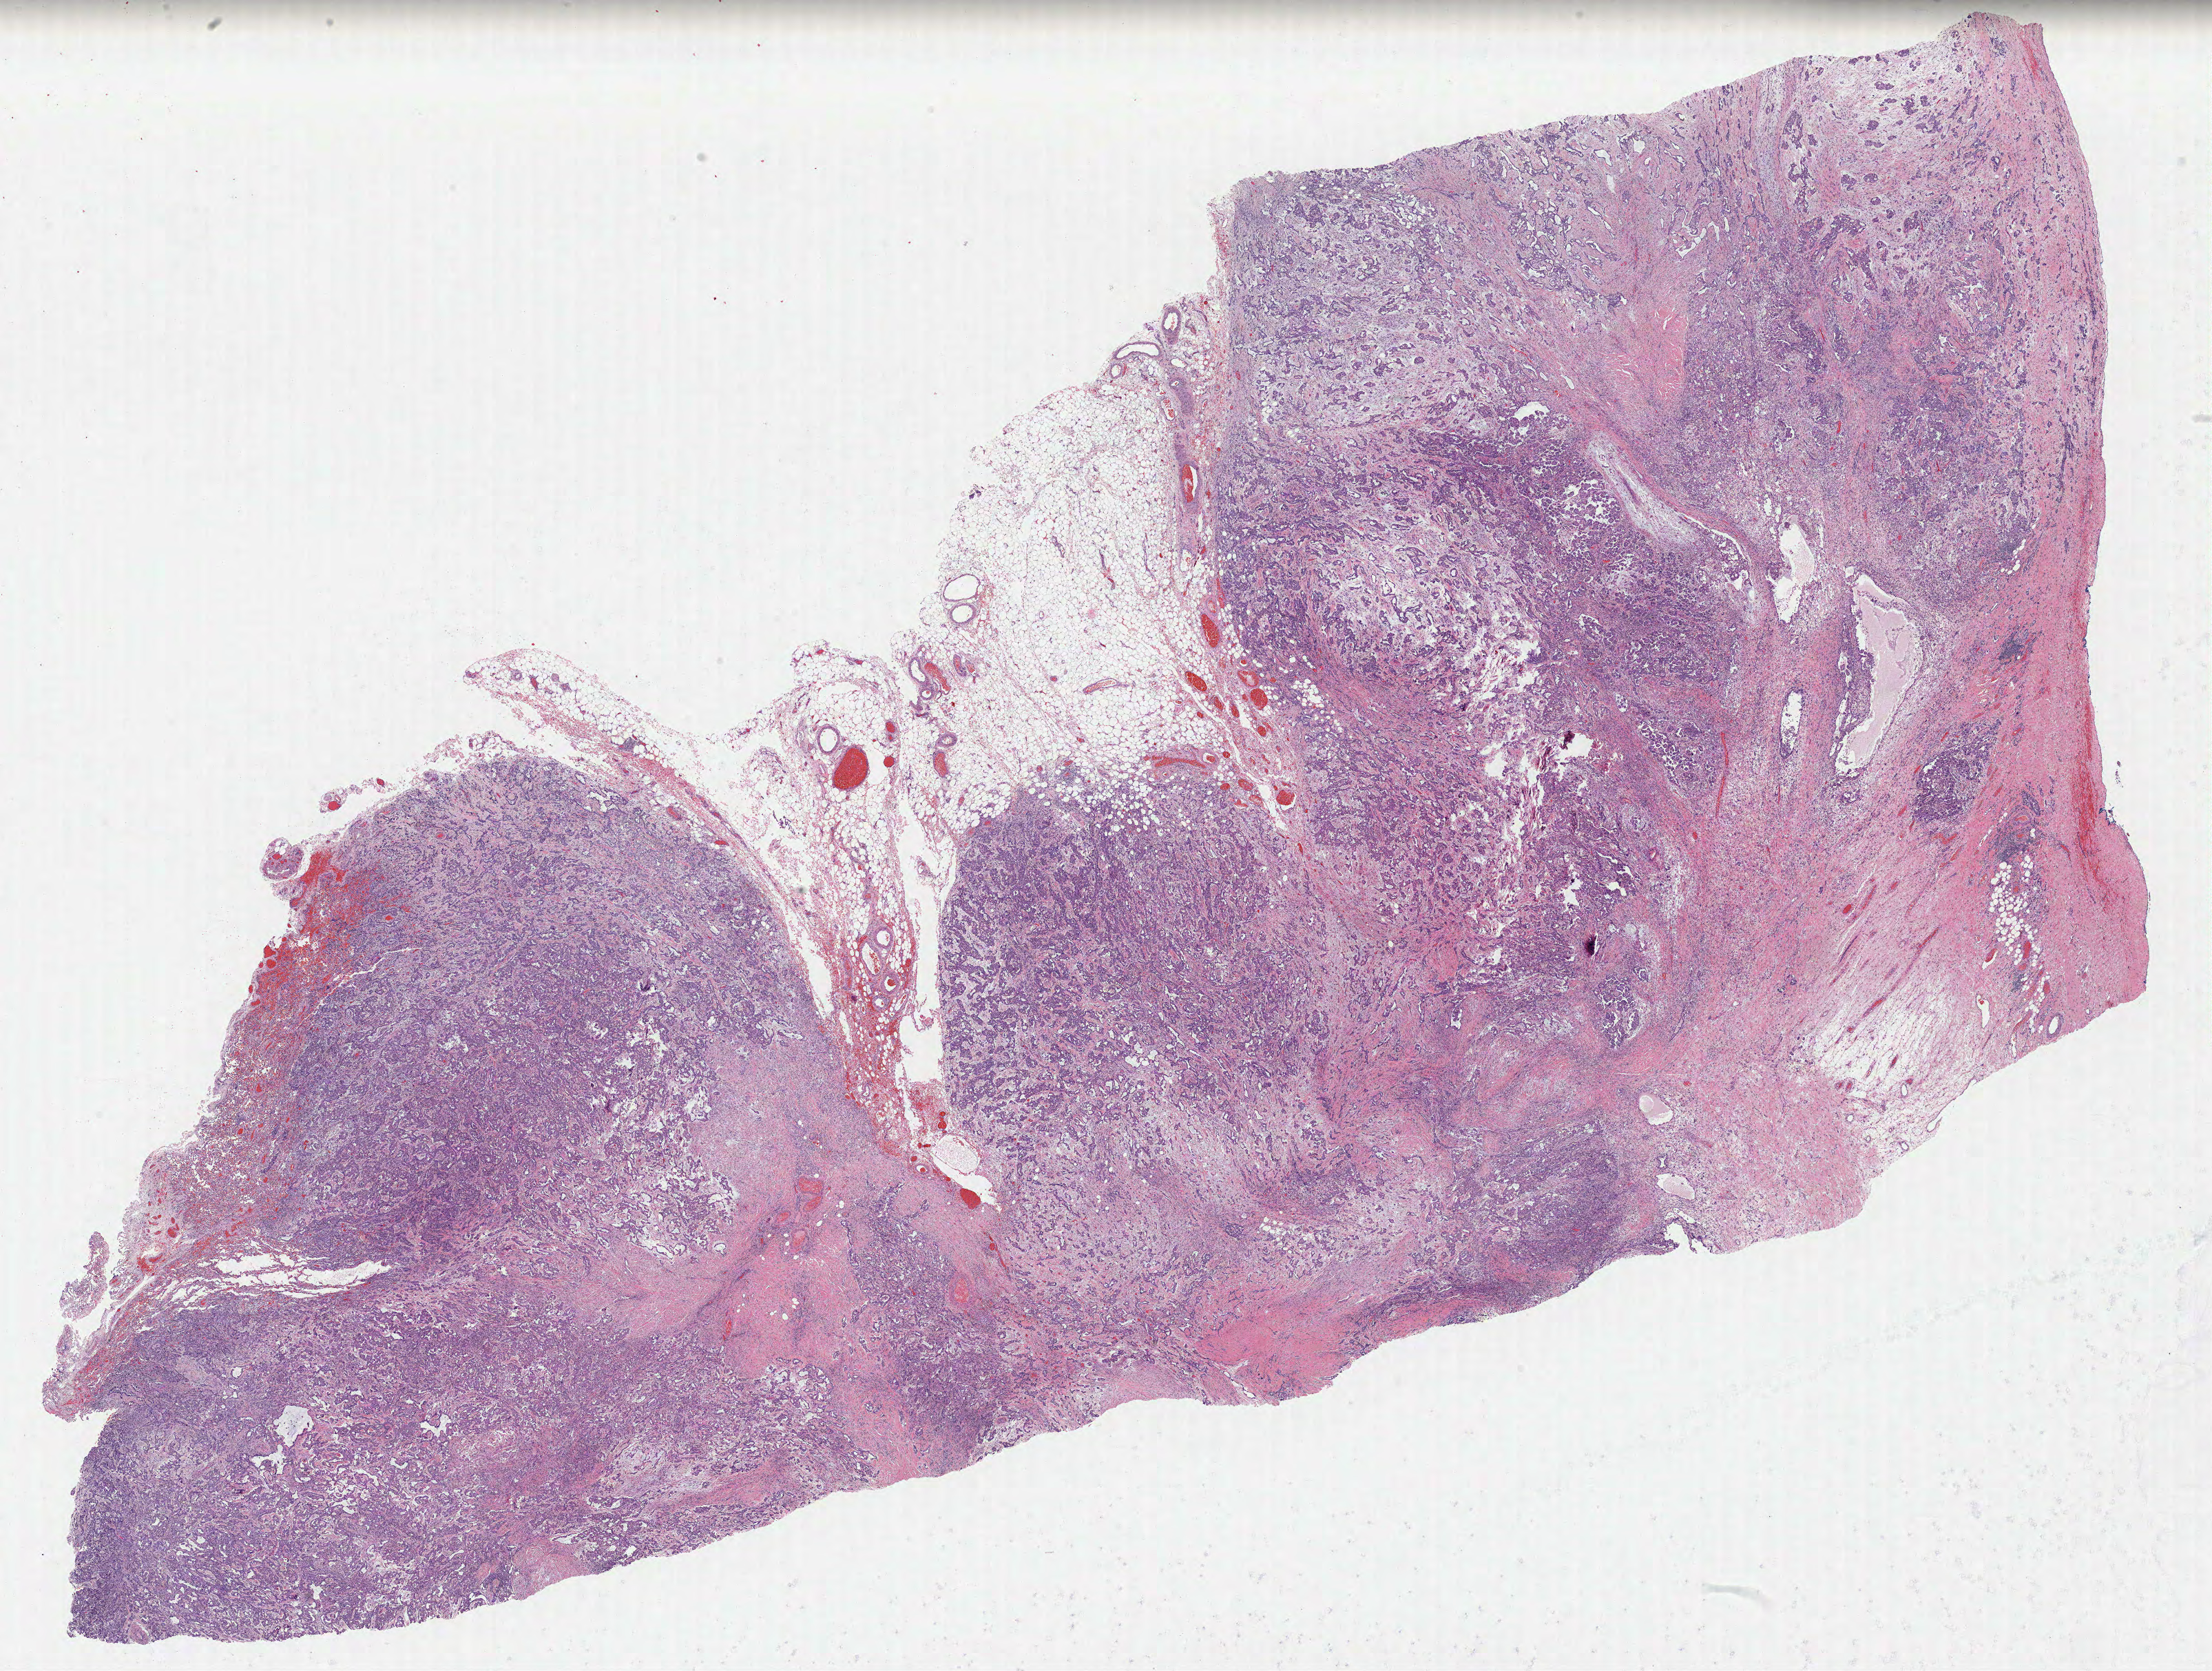
Digitized H&E tissue section (whole slide), low-resolution overview of the scanned area, about 25.6 x 19.4 mm; formalin-fixed paraffin-embedded (FFPE) diagnostic section; sample: primary tumour, mesothelium. Male, age 68 years at initial diagnosis.
- histologic diagnosis: Mesothelioma, biphasic, malignant (pleura, NOS)
- AJCC pathologic stage: IV (7th edition)
- laterality: left
- TNM: T4 N3 M0